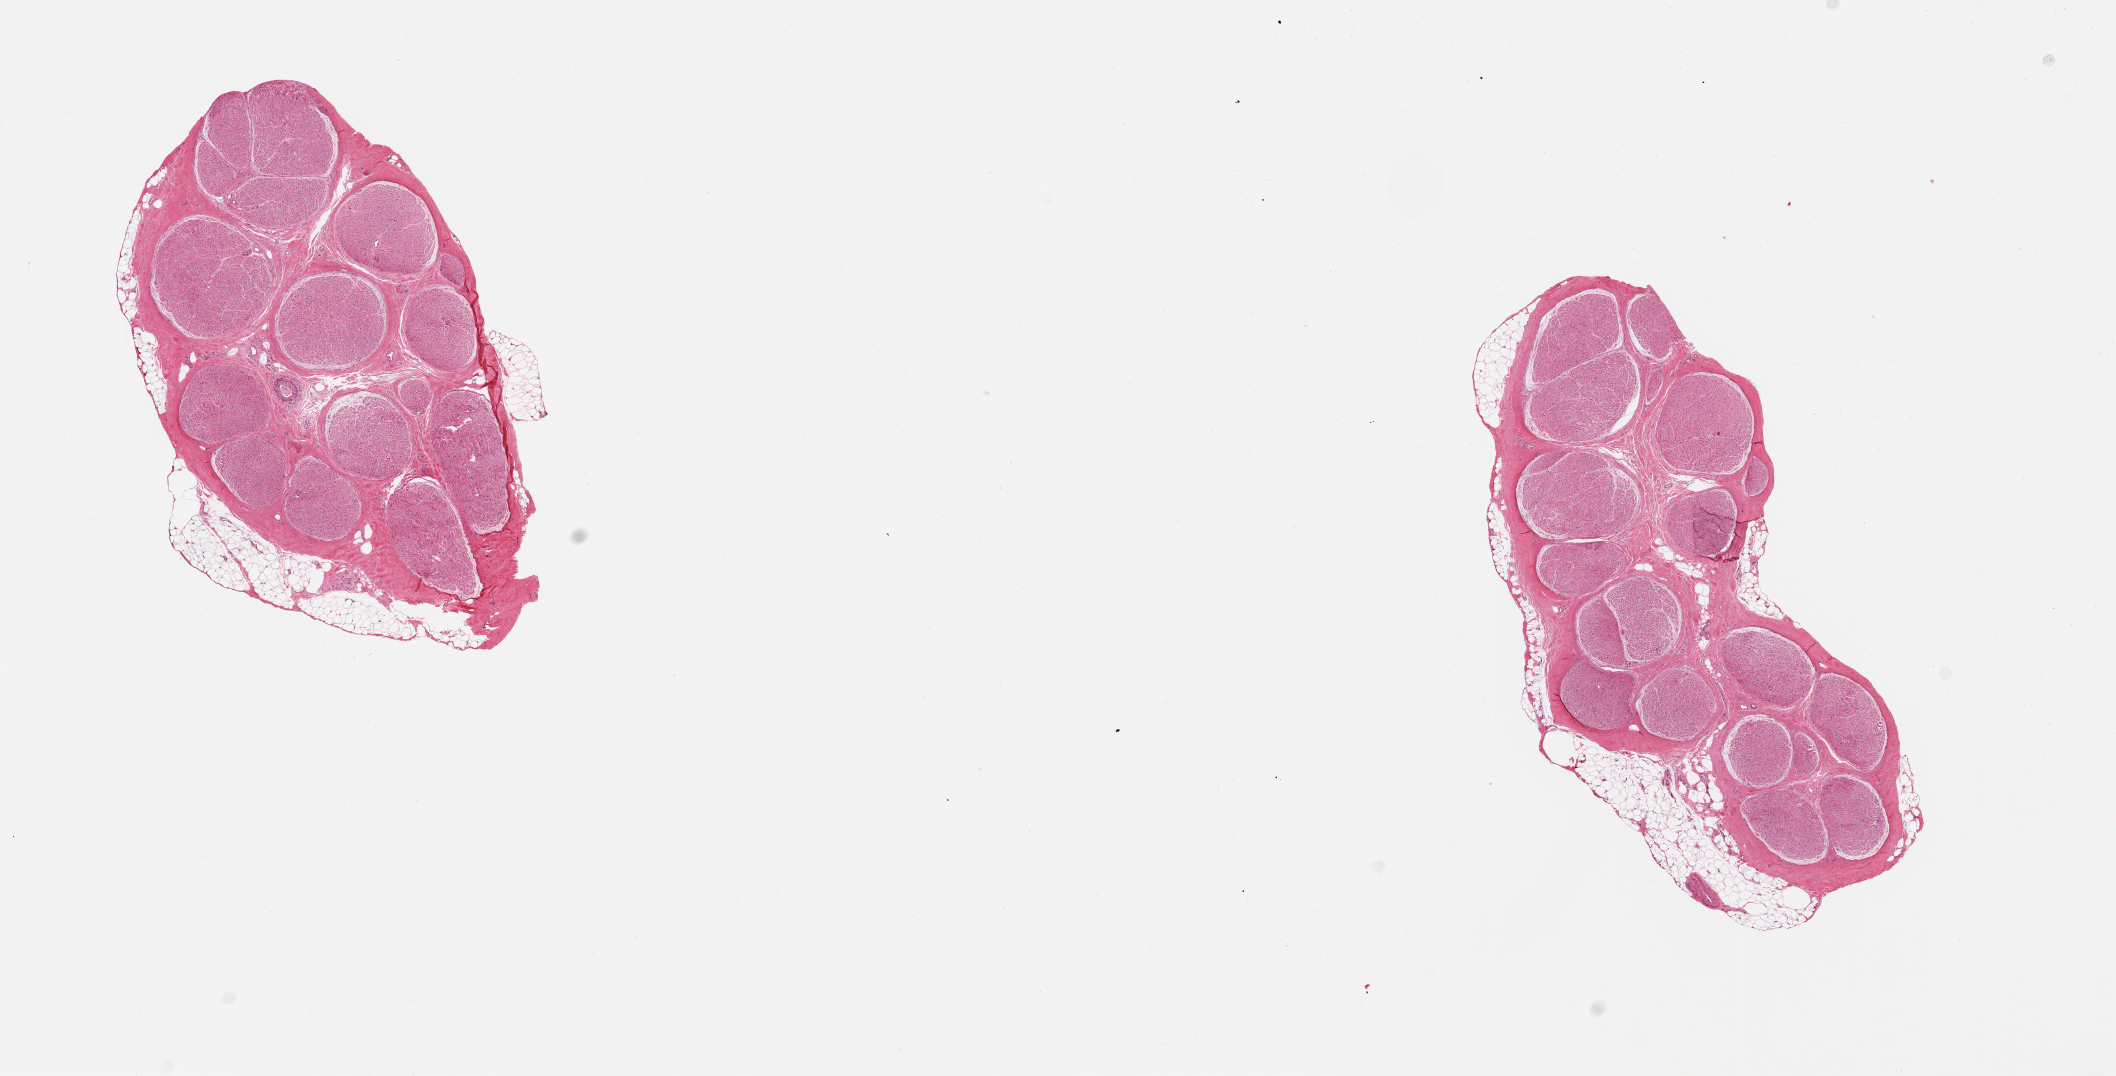
Haematoxylin and eosin whole-slide image, brightfield — shown as a low-resolution overview of the whole scanned area (about 16.7 x 8.5 mm), PAXgene-fixed, paraffin-embedded tissue, target tissue: tibial nerve, tissue donor sample. Donor: male.
Review note (as recorded): 2 pieces; 5x3 & 5x3mm; discontinuous adherent fat ~0.5mm.